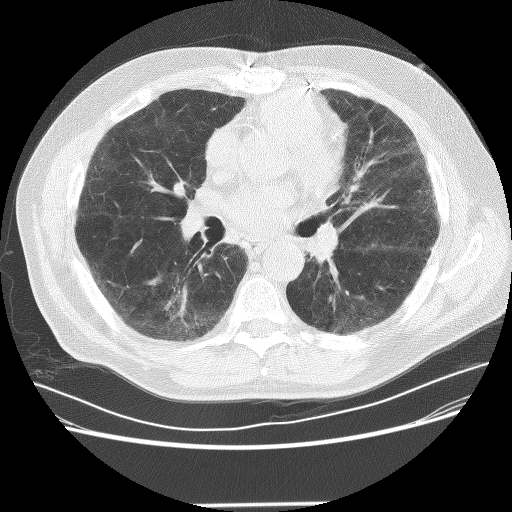
Axial slice from a low-dose chest CT screening exam. Baseline screening round. Lung window (W 1500 / L -600 HU). 2.5 mm slice thickness. Lung (sharp) reconstruction kernel (BONE). 120 kVp. Slice 128 of 281 in the series. Male participant, aged 72 years at enrolment.
Expert-annotated lung lesion, bounding box <142,269,203,323> (left, top, right, bottom; pixels). The screening reader recorded 2 non-calcified nodules or masses ≥4 mm on this exam (right lower lobe, left lower lobe); which of them this box marks is not recorded. Participant outcome: lung cancer diagnosed 436 days after this screen — squamous cell carcinoma, NOS, right lower lobe, poorly differentiated (G3), stage IB (AJCC 6th edition), 42 mm at pathology.